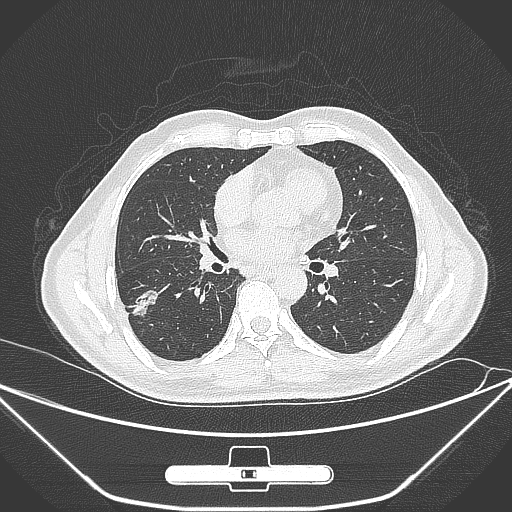
Chest CT, one axial slice; position 144 of 310 along the scan axis; 120 kVp; lung window (W 1500 / L -600 HU); 1 mm slice thickness; 512 × 512 image matrix. Patient: male, 71 years. From the clinical record (not read from this slice): clinical TNM (as recorded): T1c N0 M0; histopathological grade: G2.
Annotated regions visible in this slice (rectangle marked by the reading radiologist):
- lung tumour (recorded histology: adenocarcinoma): bounding box [x1, y1, x2, y2] px = [129, 288, 166, 326]